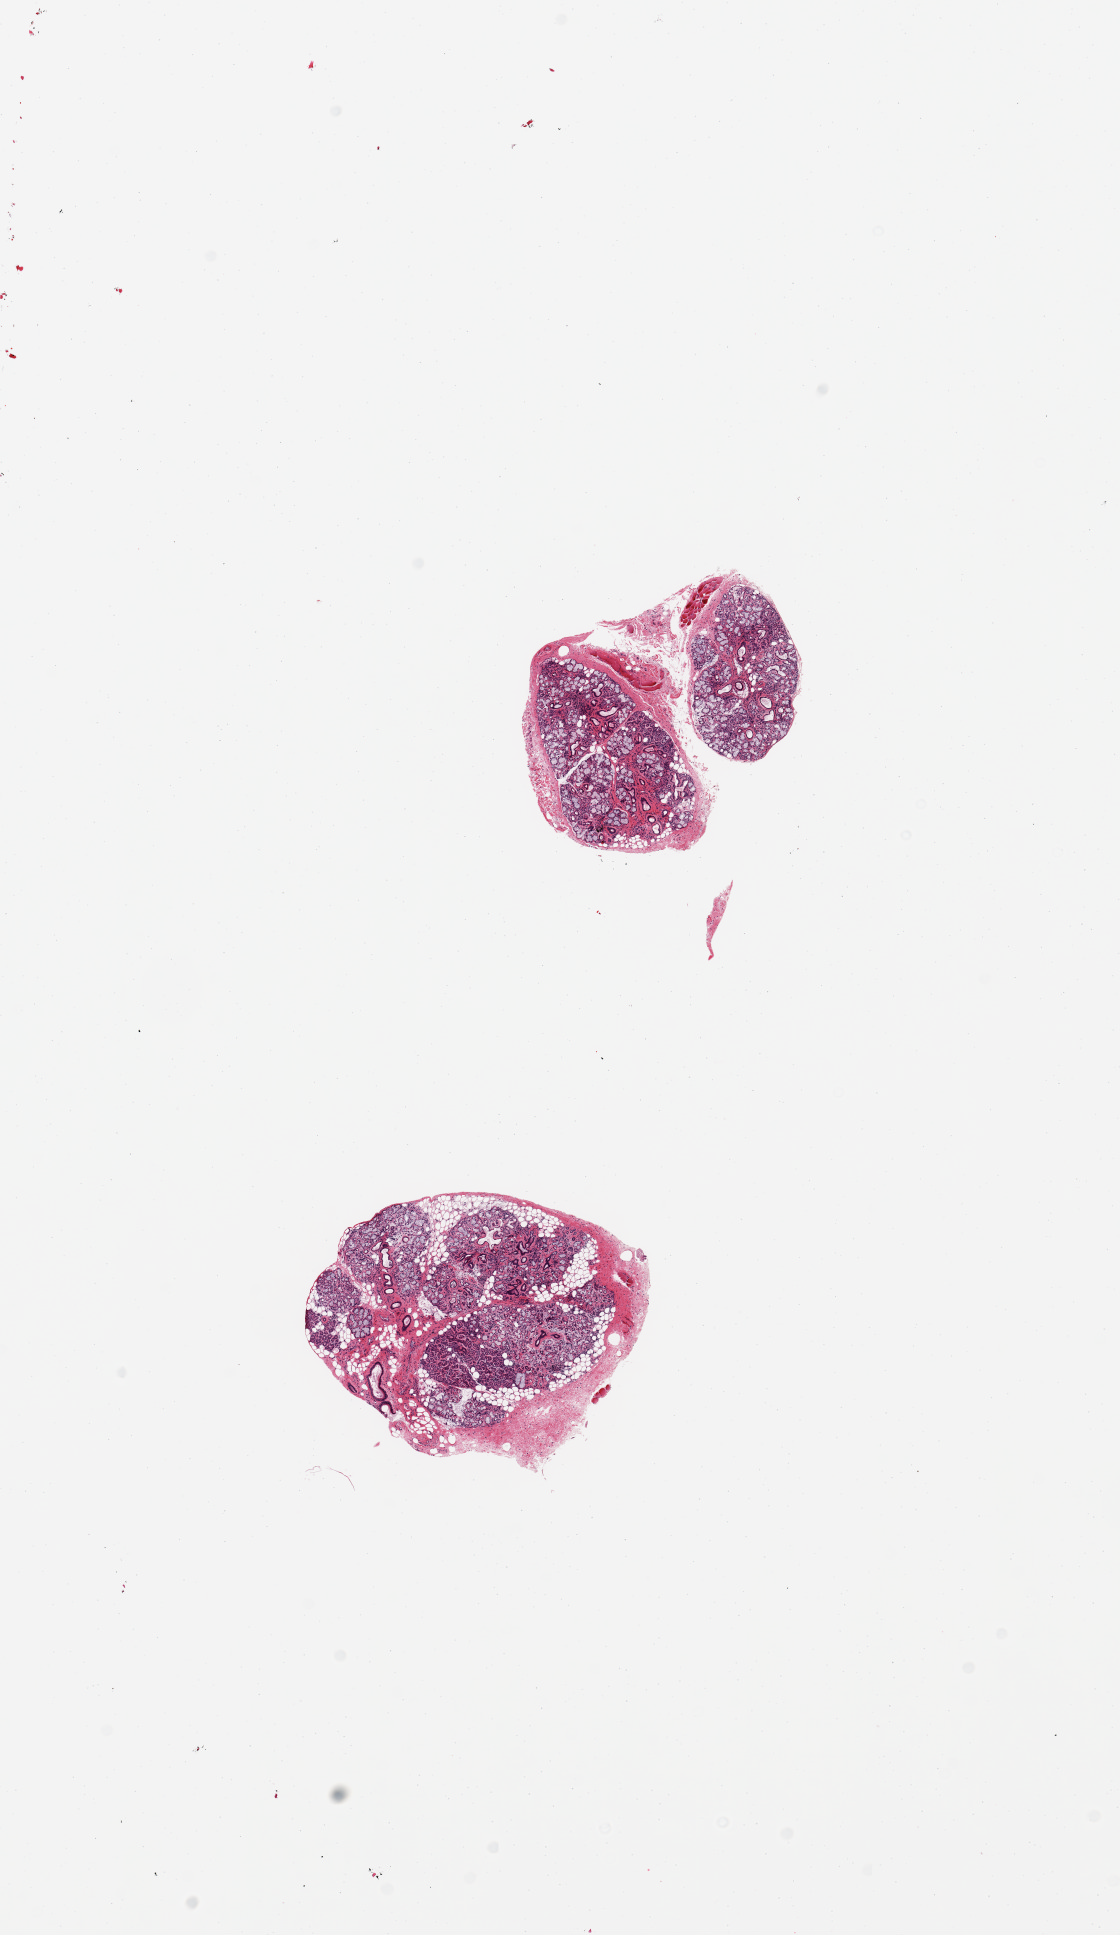
Whole-slide image, hematoxylin and eosin (H&E) stain, low-resolution overview of the scanned area, about 8.9 x 15.3 mm (slide scanned at 20x); PAXgene-fixed paraffin-embedded (PFPE) section; target tissue: minor salivary gland; tissue donor sample. Donor sex: male.
Pathologist's review note for this sample: 3 pieces, glandular elements are ~80-90% total tissue, good specimens.